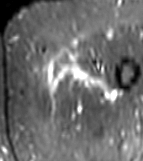
MRI of an extremity soft-tissue mass, one axial slice; STIR; MR volume resampled by the dataset authors to the PET/CT grid (not the native acquisition matrix); 3.27 mm slice thickness; 143 × 161 image matrix, field of view 140 × 157 mm. Female patient. Case-level facts recorded for this patient, not image findings: histological type: myxofibrosarcoma; grade: intermediate; site of the primary tumour: left thigh.
Structures marked on this image (expert contour drawn on MRI and transferred to this co-registered scan by the dataset authors):
- gross tumour volume including surrounding oedema: box from (x=38, y=56) to (x=111, y=98) px